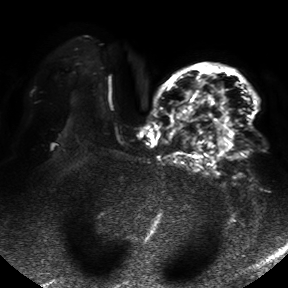
Breast MRI, one axial slice; slice 31 of 50 in the series (ordered by position); diffusion-weighted series; image 2 of 4 stored at this slice position (different b-values; order by instance number); 1.5 T; 4 mm slice thickness; 288 × 288 image matrix. Female patient.
Outlined on this slice (outlined manually by an expert reader):
- tumour on diffusion-weighted imaging: bounding box <185,113,234,152> (left, top, right, bottom; pixels)